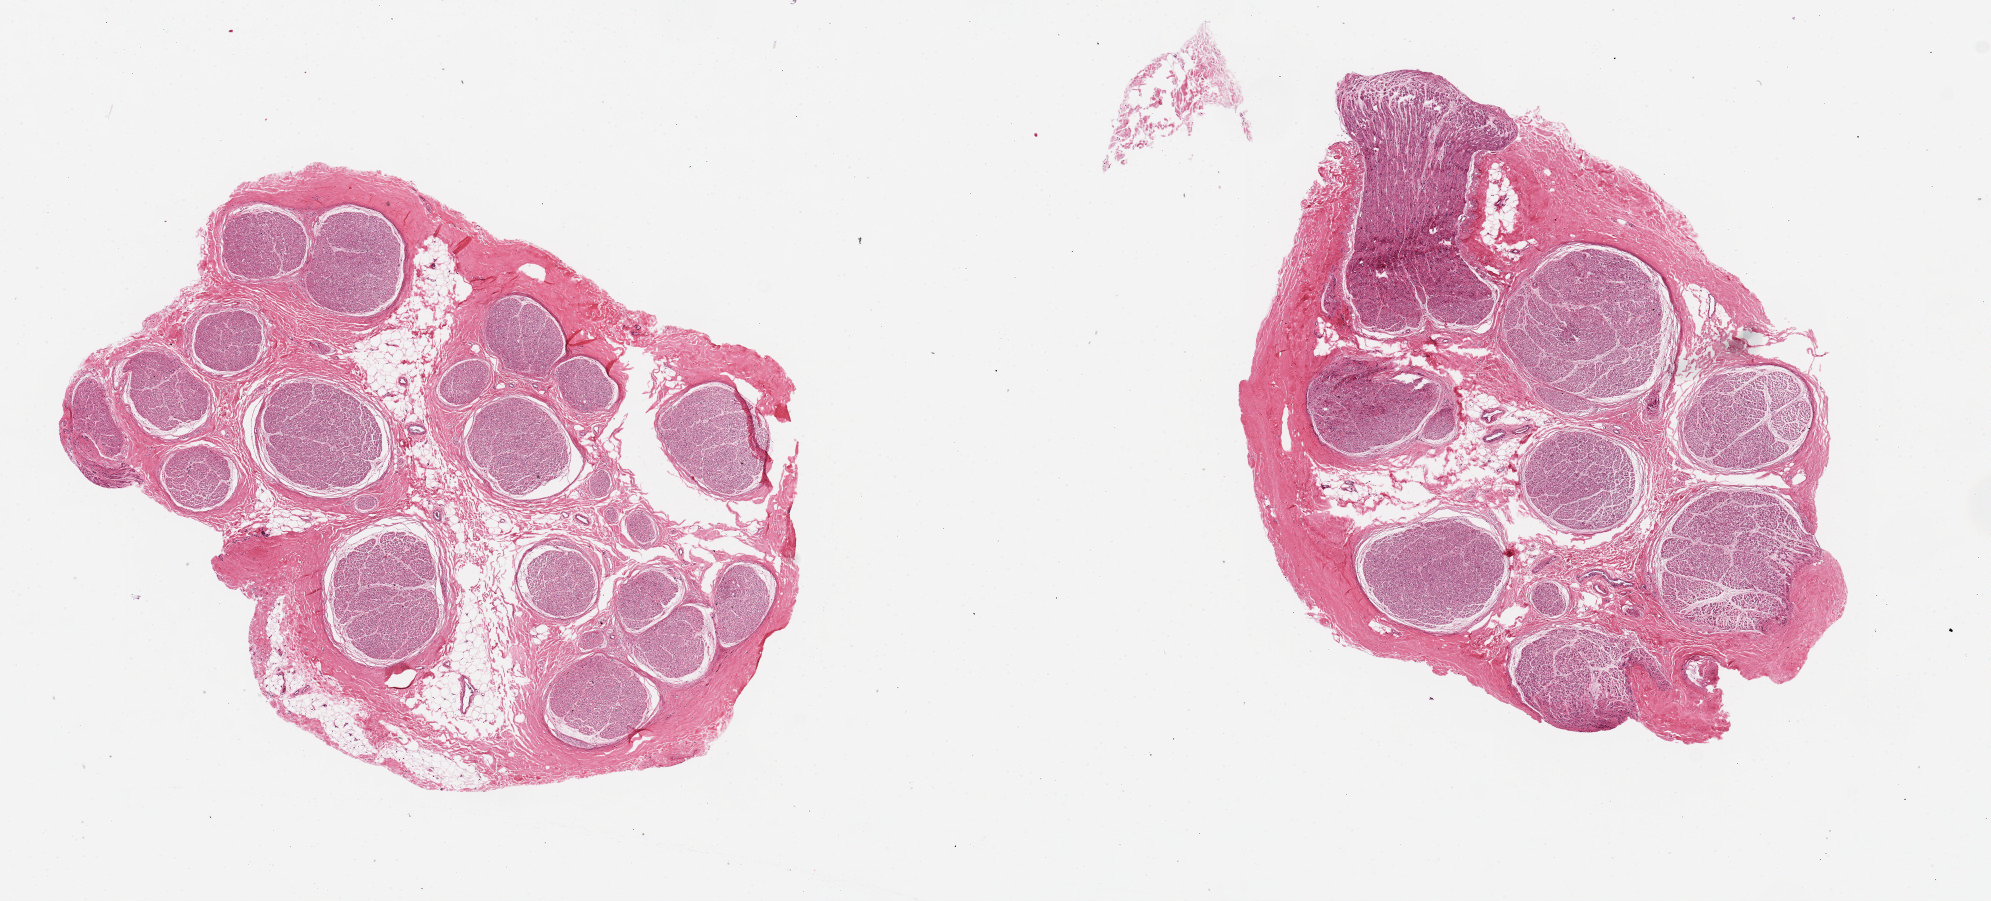
Digitized H&E-stained section, brightfield, whole scanned area (about 15.8 x 7.1 mm) shown as a low-resolution overview, PAXgene-fixed, paraffin-embedded tissue, sampled site (target tissue): tibial nerve, donor tissue sample. Donor sex: male.
Pathologist's review note for this sample: 2 pieces ~5mm d. Clean specimen; interstital fat/fibrous tissue is ~15% of specimen.